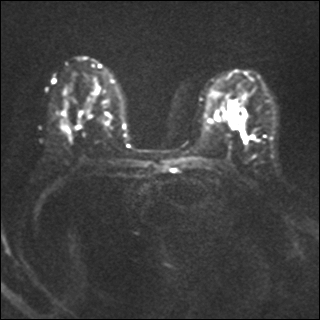
Breast MRI, one axial slice. Position 24 of 40 along the scan axis. Diffusion-weighted series; image 2 of 4 stored at this slice position (different b-values; order by instance number). 1.5 T. 4 mm slice thickness. 320 × 320 image matrix, field of view 320 × 320 mm. Female patient.
Structures marked on this image (outlined manually by an expert reader):
- tumour on diffusion-weighted imaging: bounding box [x1, y1, x2, y2] px = [233, 106, 240, 113]